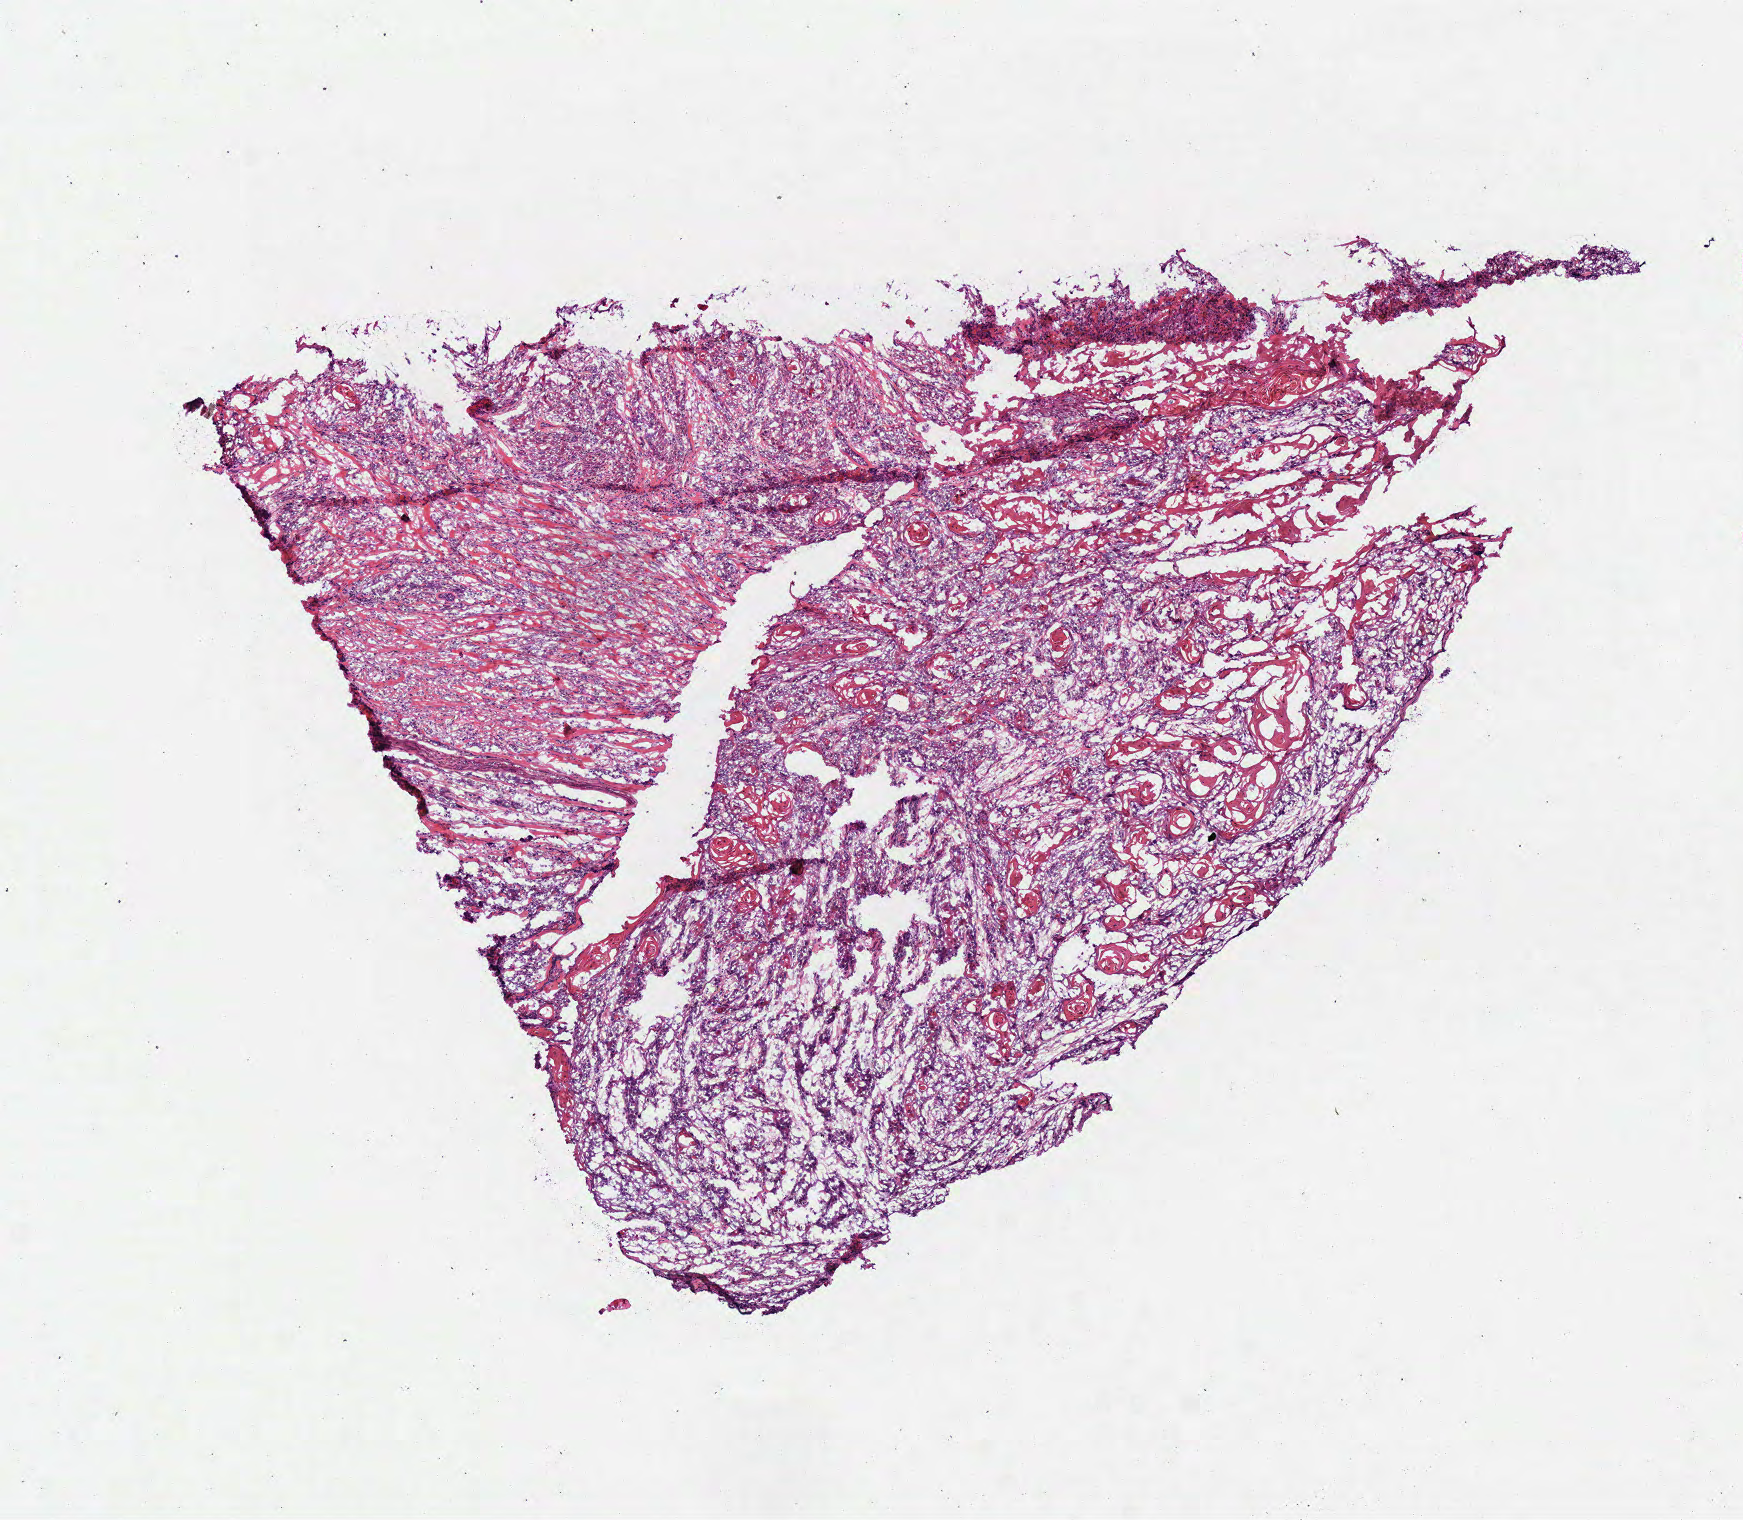
H&E whole-slide image, low-resolution overview of the scanned area, about 6.9 x 6.0 mm (acquisition: 40x scan); frozen section from the top of the tissue portion; primary tumour sample from the head and neck. Patient: male, age at initial diagnosis 53 years. Histologic grade: G3 (poorly differentiated). Pathologist review of this section (percent, as recorded): tumour cells 90%, tumour nuclei 80%, normal cells 0%, stromal cells 10%, necrosis 0%.
* AJCC pathologic stage: II (7th edition)
* pathologic diagnosis: Squamous cell carcinoma, NOS (overlapping lesion of lip, oral cavity and pharynx)
* TNM: T2 NX